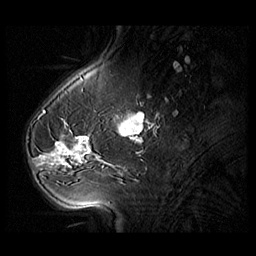
Breast MRI (dynamic contrast-enhanced), one sagittal slice. Slice 31 of 104 in the series (ordered by position). 3 images stored at this slice position (order not interpretable as contrast timing). 1.5 T. TE 1.3 ms, TR 5.5 ms. 3 mm slice thickness. 256 × 256 image matrix, field of view 220 × 220 mm. Patient: female, 54 years. Case-level facts recorded for this patient, not image findings: setting: breast cancer imaged before/during neoadjuvant chemotherapy; receptor status: HR-positive, HER2-negative.
Outlined on this slice (semi-automatic segmentation, software-assisted and operator-edited):
- analysis volume of interest (the breast-tissue region the enhancement analysis was run in; not a lesion): bounding box (x1, y1, x2, y2) in pixels: (28, 127, 104, 182)
- tumour enhancement mask (voxels above the 140 % enhancement threshold inside the analysis volume of interest): (38, 135, 90, 165)